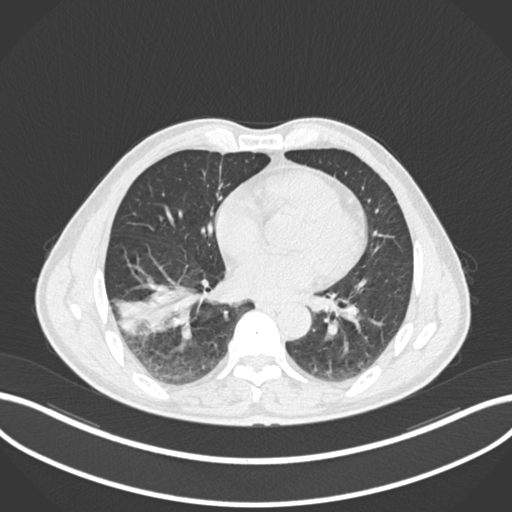
Chest CT, one axial slice; 120 kVp; lung window (W 1500 / L -600 HU); 512 × 512 image matrix. Patient: male, 58 years. From the clinical record (not read from this slice): clinical TNM (as recorded): T3 N0 M0; histopathological grade: G2.
Annotated regions visible in this slice (rectangle marked by the reading radiologist):
- lung tumour (recorded histology: squamous cell carcinoma): bounding box [x1, y1, x2, y2] px = [112, 275, 209, 337]